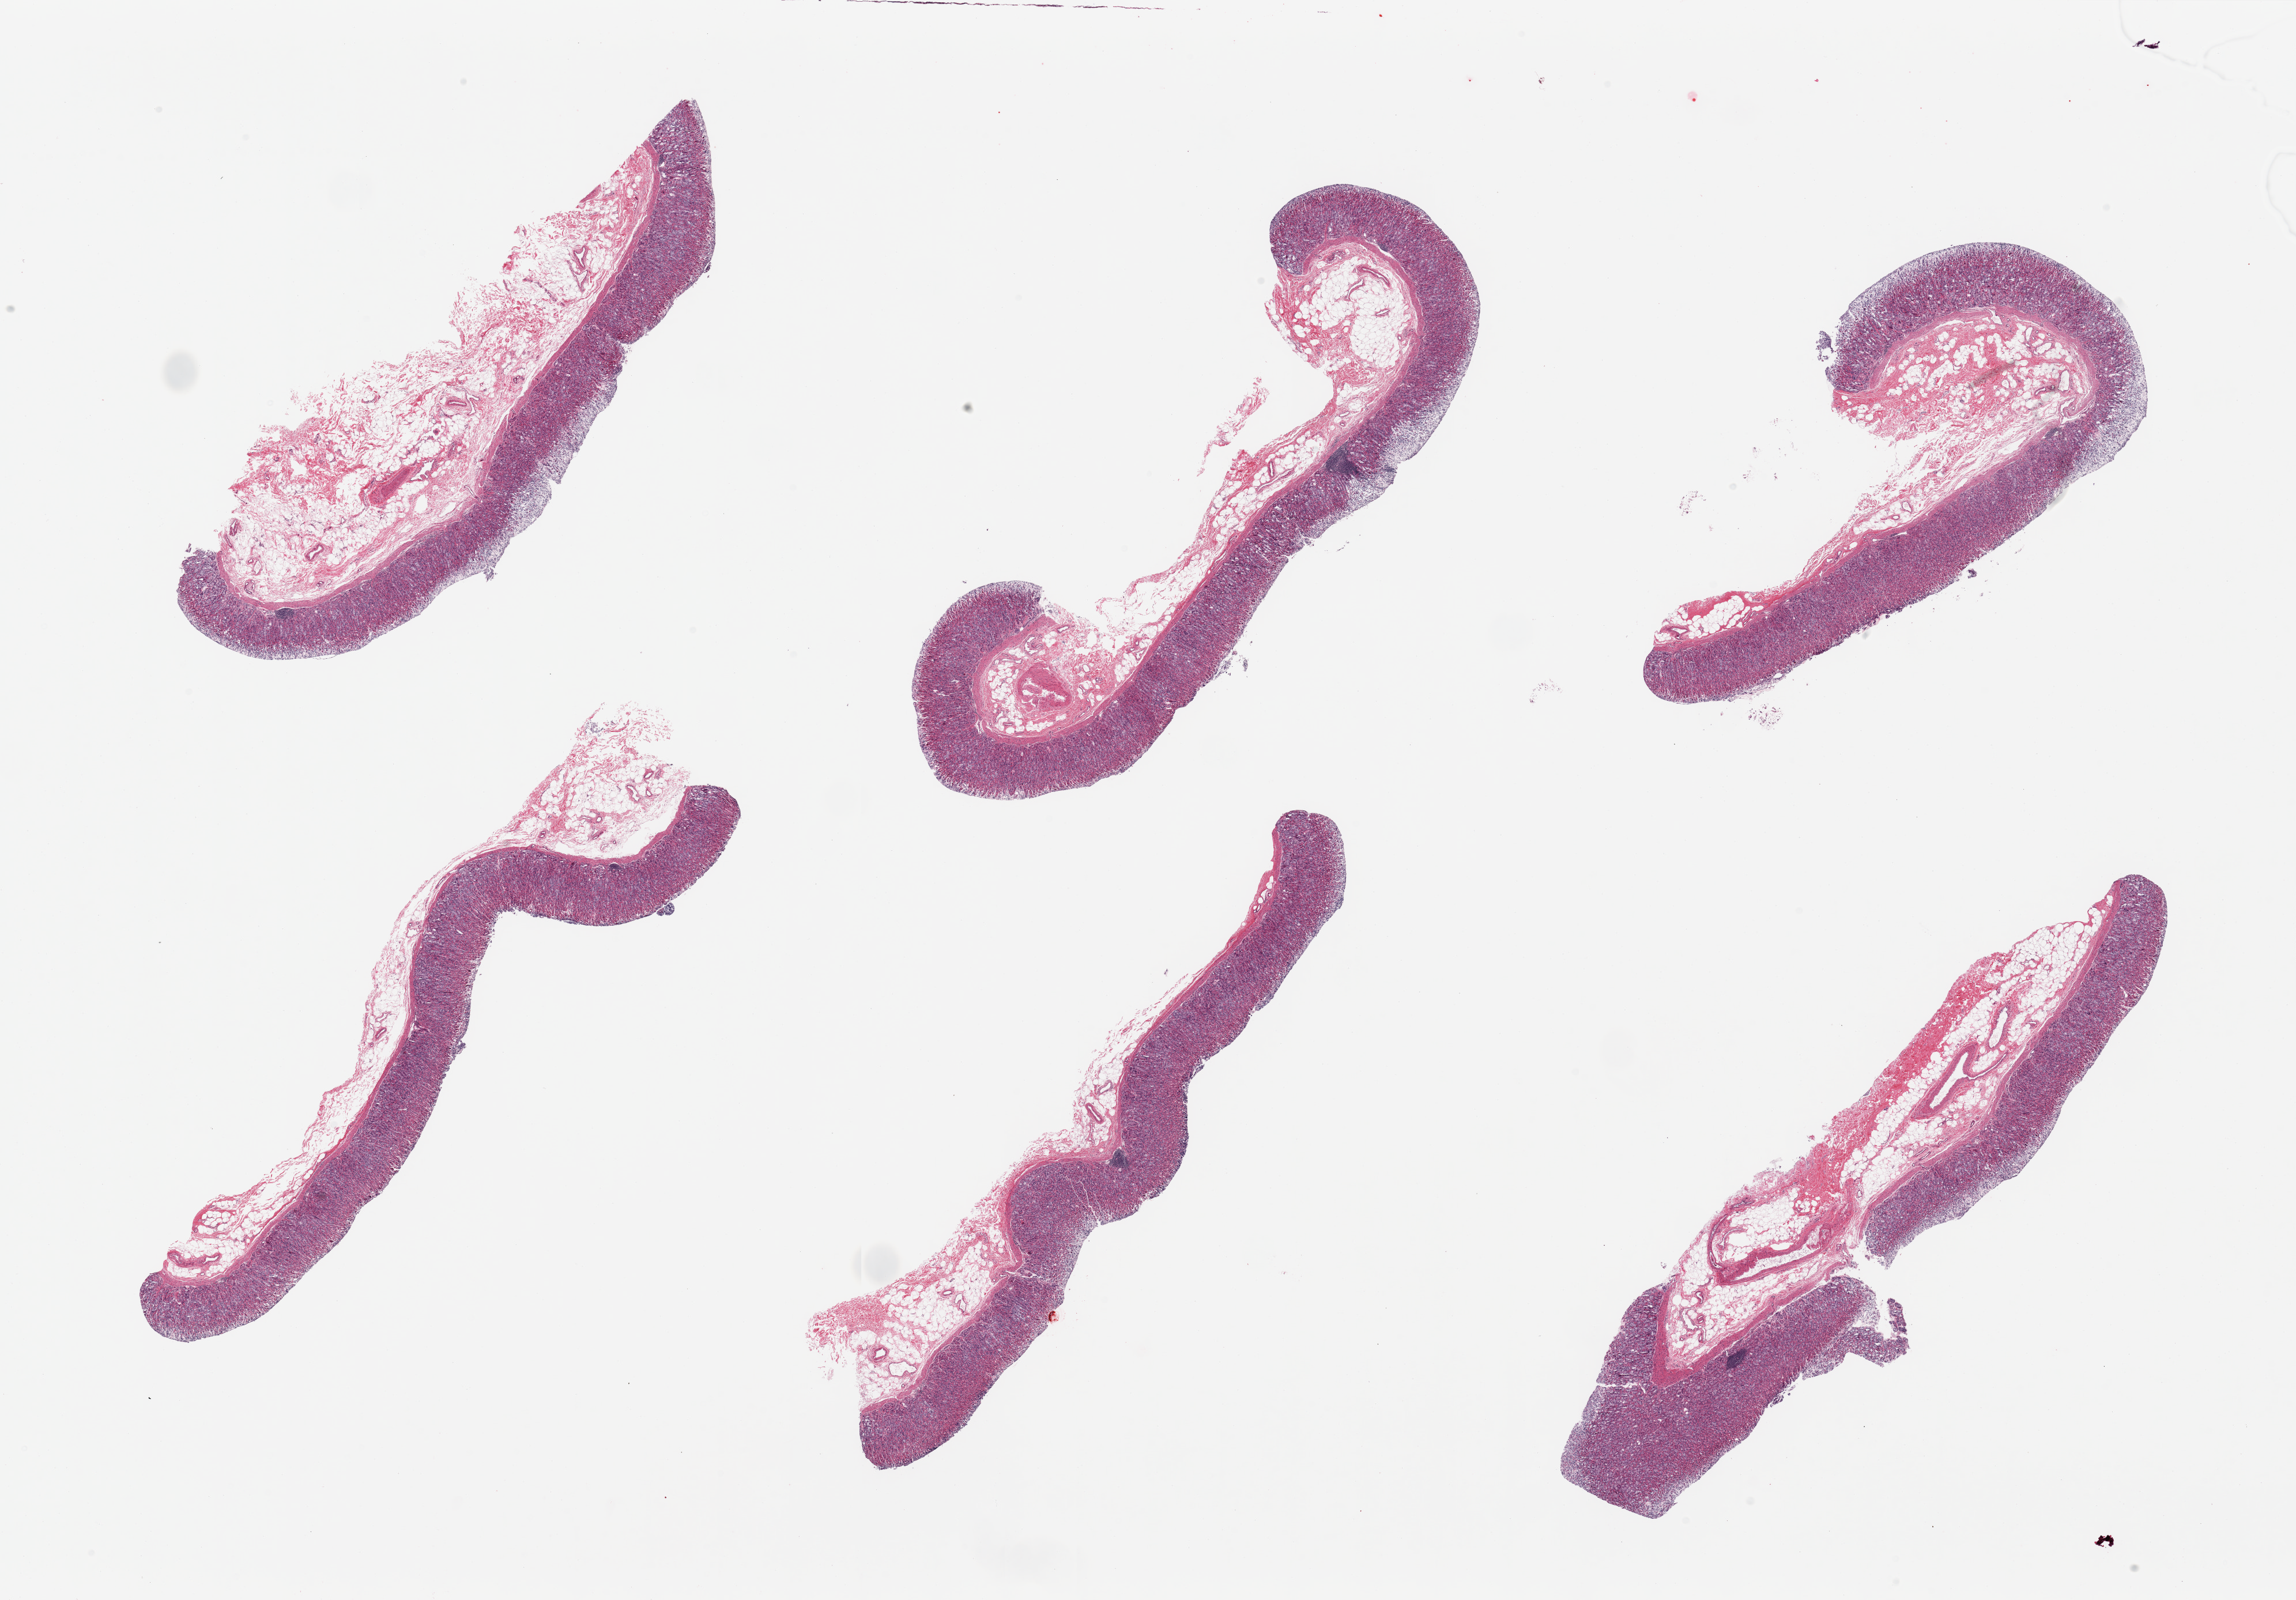
Digitized H&E-stained section, a low-resolution overview of the entire scanned area, about 31.5 x 22.0 mm (acquisition: 20x scan). PAXgene-fixed, paraffin-embedded tissue. Target tissue: stomach. Tissue donor sample. Donor: male.
- review note (as recorded): 6 pieces; well preserved oxyntic glands, sloughed foveolar (surface) epithelium; no muscularis propria